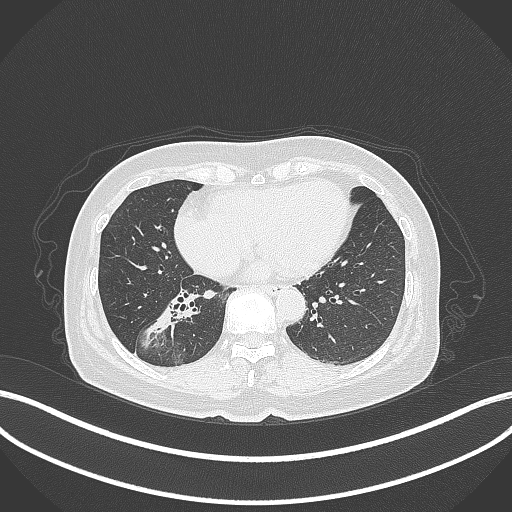
Chest CT, one axial slice. Position 147 of 429 along the scan axis. Reconstruction kernel B70f. 120 kVp. Lung window (W 1500 / L -600 HU). 1 mm slice thickness. 512 × 512 image matrix, field of view 400 × 400 mm. Patient: female, 67 years. Case-level facts recorded for this patient, not image findings: clinical TNM (as recorded): T1c N1 M0; histopathological grade: G2-3.
Annotated regions visible in this slice (bounding box drawn by a radiologist):
- lung tumour (recorded histology: adenocarcinoma): bounding box (x1, y1, x2, y2) in pixels: (138, 289, 197, 342)